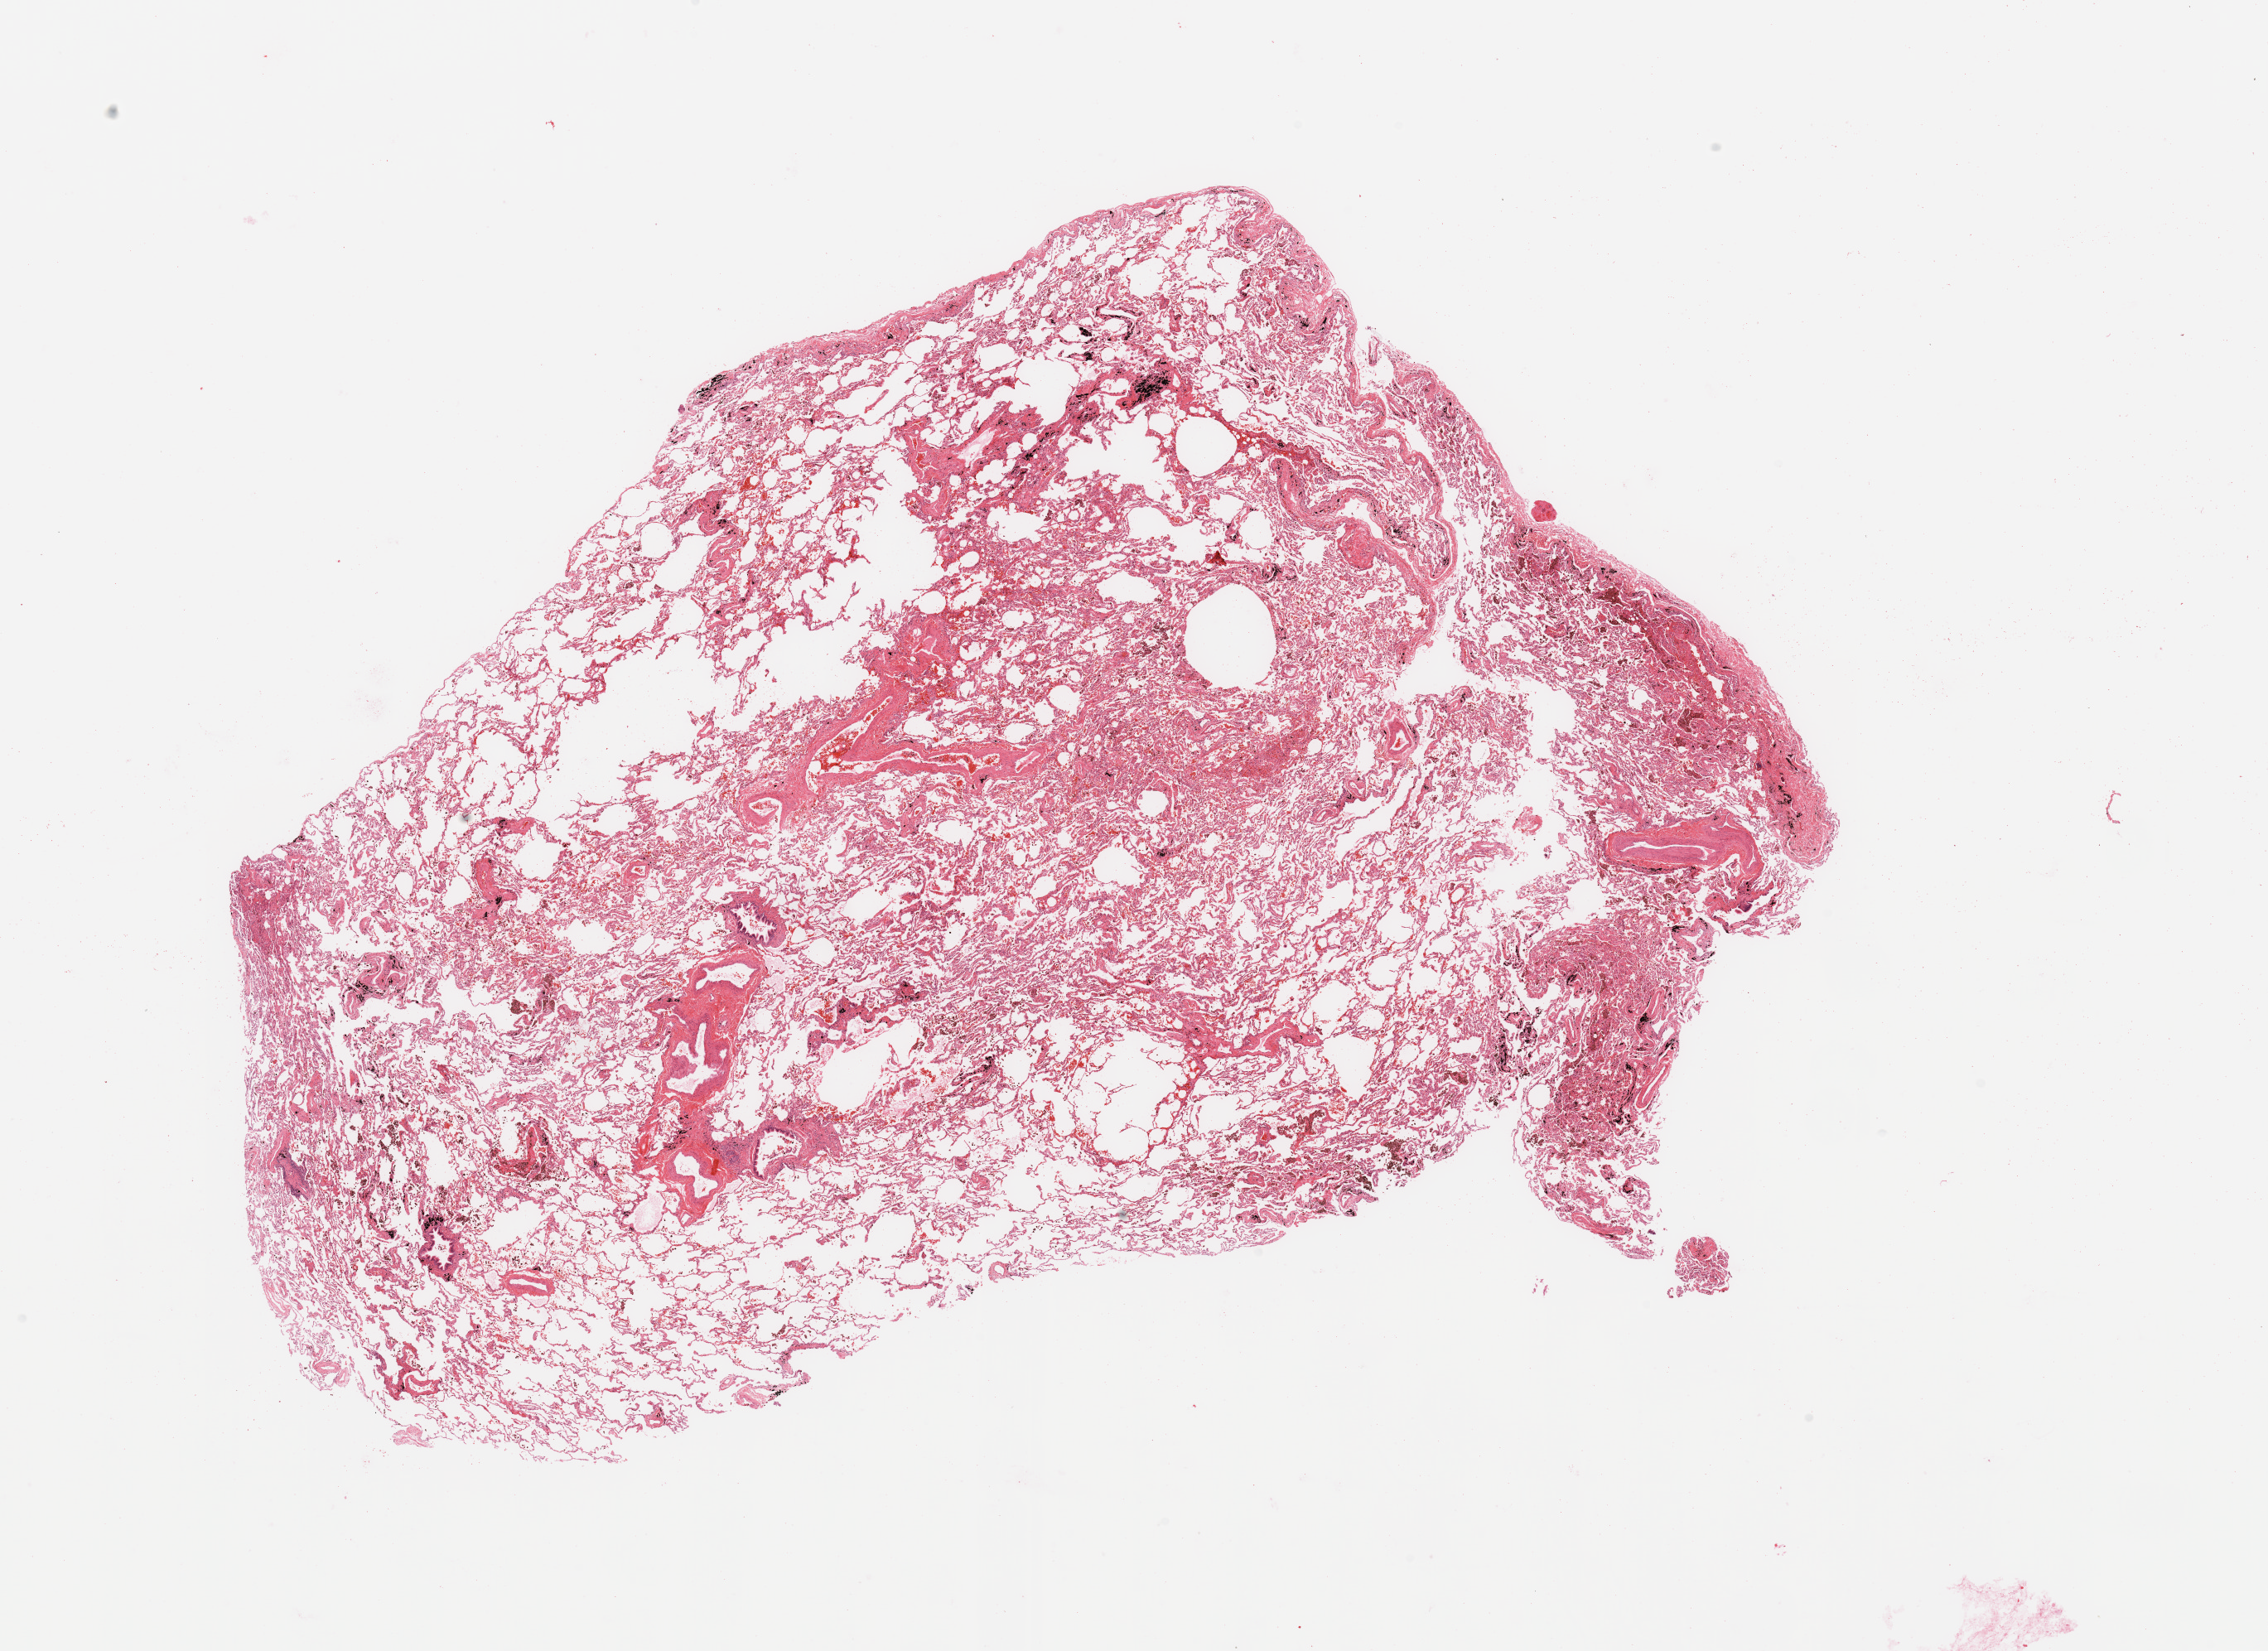
H&E whole-slide image — low-resolution overview of the scanned area, about 21.7 x 15.8 mm (acquisition: 20x scan); normal (non-tumour) tissue sample, sampled site: lung. Male, 59 y/o.
• this section: normal (non-tumour) tissue from the same patient
• patient diagnosis: Adenocarcinoma, NOS